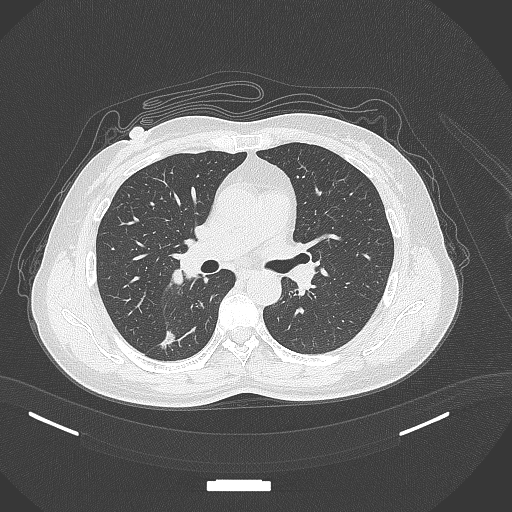
Chest CT, one axial slice. Slice 177 of 352 in the series (ordered by position). Reconstruction kernel B70f. 120 kVp. Lung window (W 1500 / L -600 HU). 512 × 512 image matrix, field of view 400 × 400 mm. Female patient, age 55 years. From the clinical record (not read from this slice): clinical TNM (as recorded): T1c N1 M0.
Annotated regions visible in this slice (rectangle marked by the reading radiologist):
- lung tumour (recorded histology: adenocarcinoma): bounding box (x1, y1, x2, y2) in pixels: (158, 325, 180, 352)